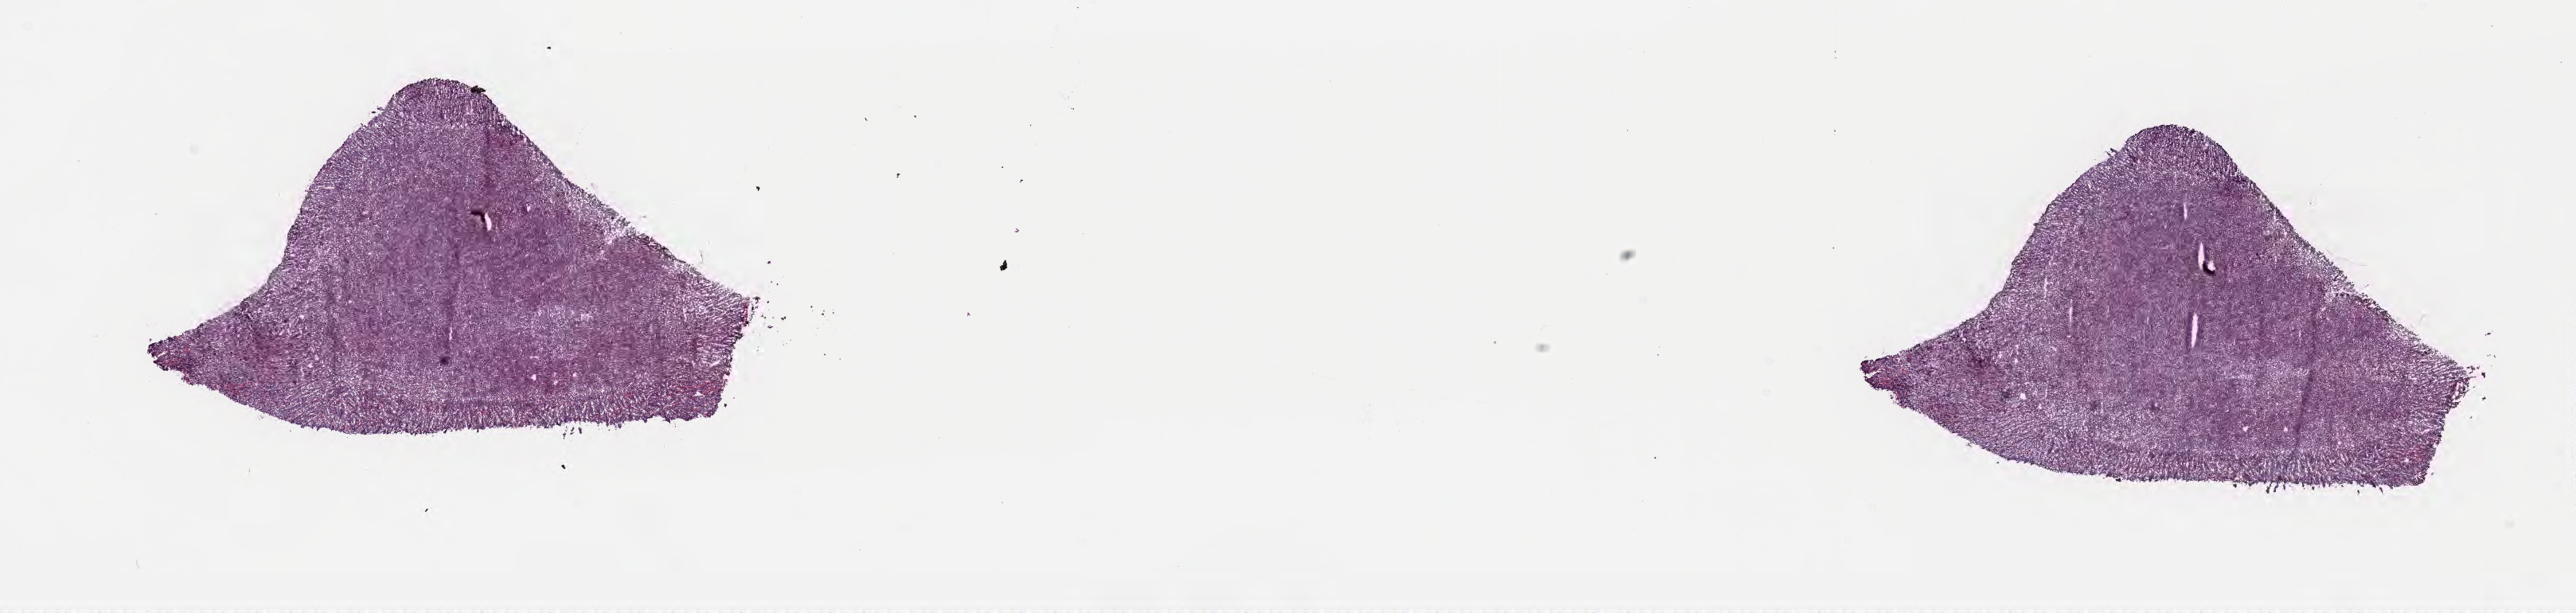
Haematoxylin and eosin whole-slide image, low-resolution overview of the scanned area, about 26.2 x 6.2 mm. Frozen section. Primary tumor. Site: mandible. Patient: female, age at initial diagnosis 5 years. Slide review estimates, as recorded: tumor cells 90%, tumor nuclei 90%, stromal cells 5%, necrosis 5%, normal cells 0%. Infiltration values recorded for this section: lymphocyte infiltration 50%, monocyte infiltration 25%, neutrophil infiltration 0%.
- histologic diagnosis: Burkitt lymphoma, NOS
- Ann Arbor stage (patient): Stage III